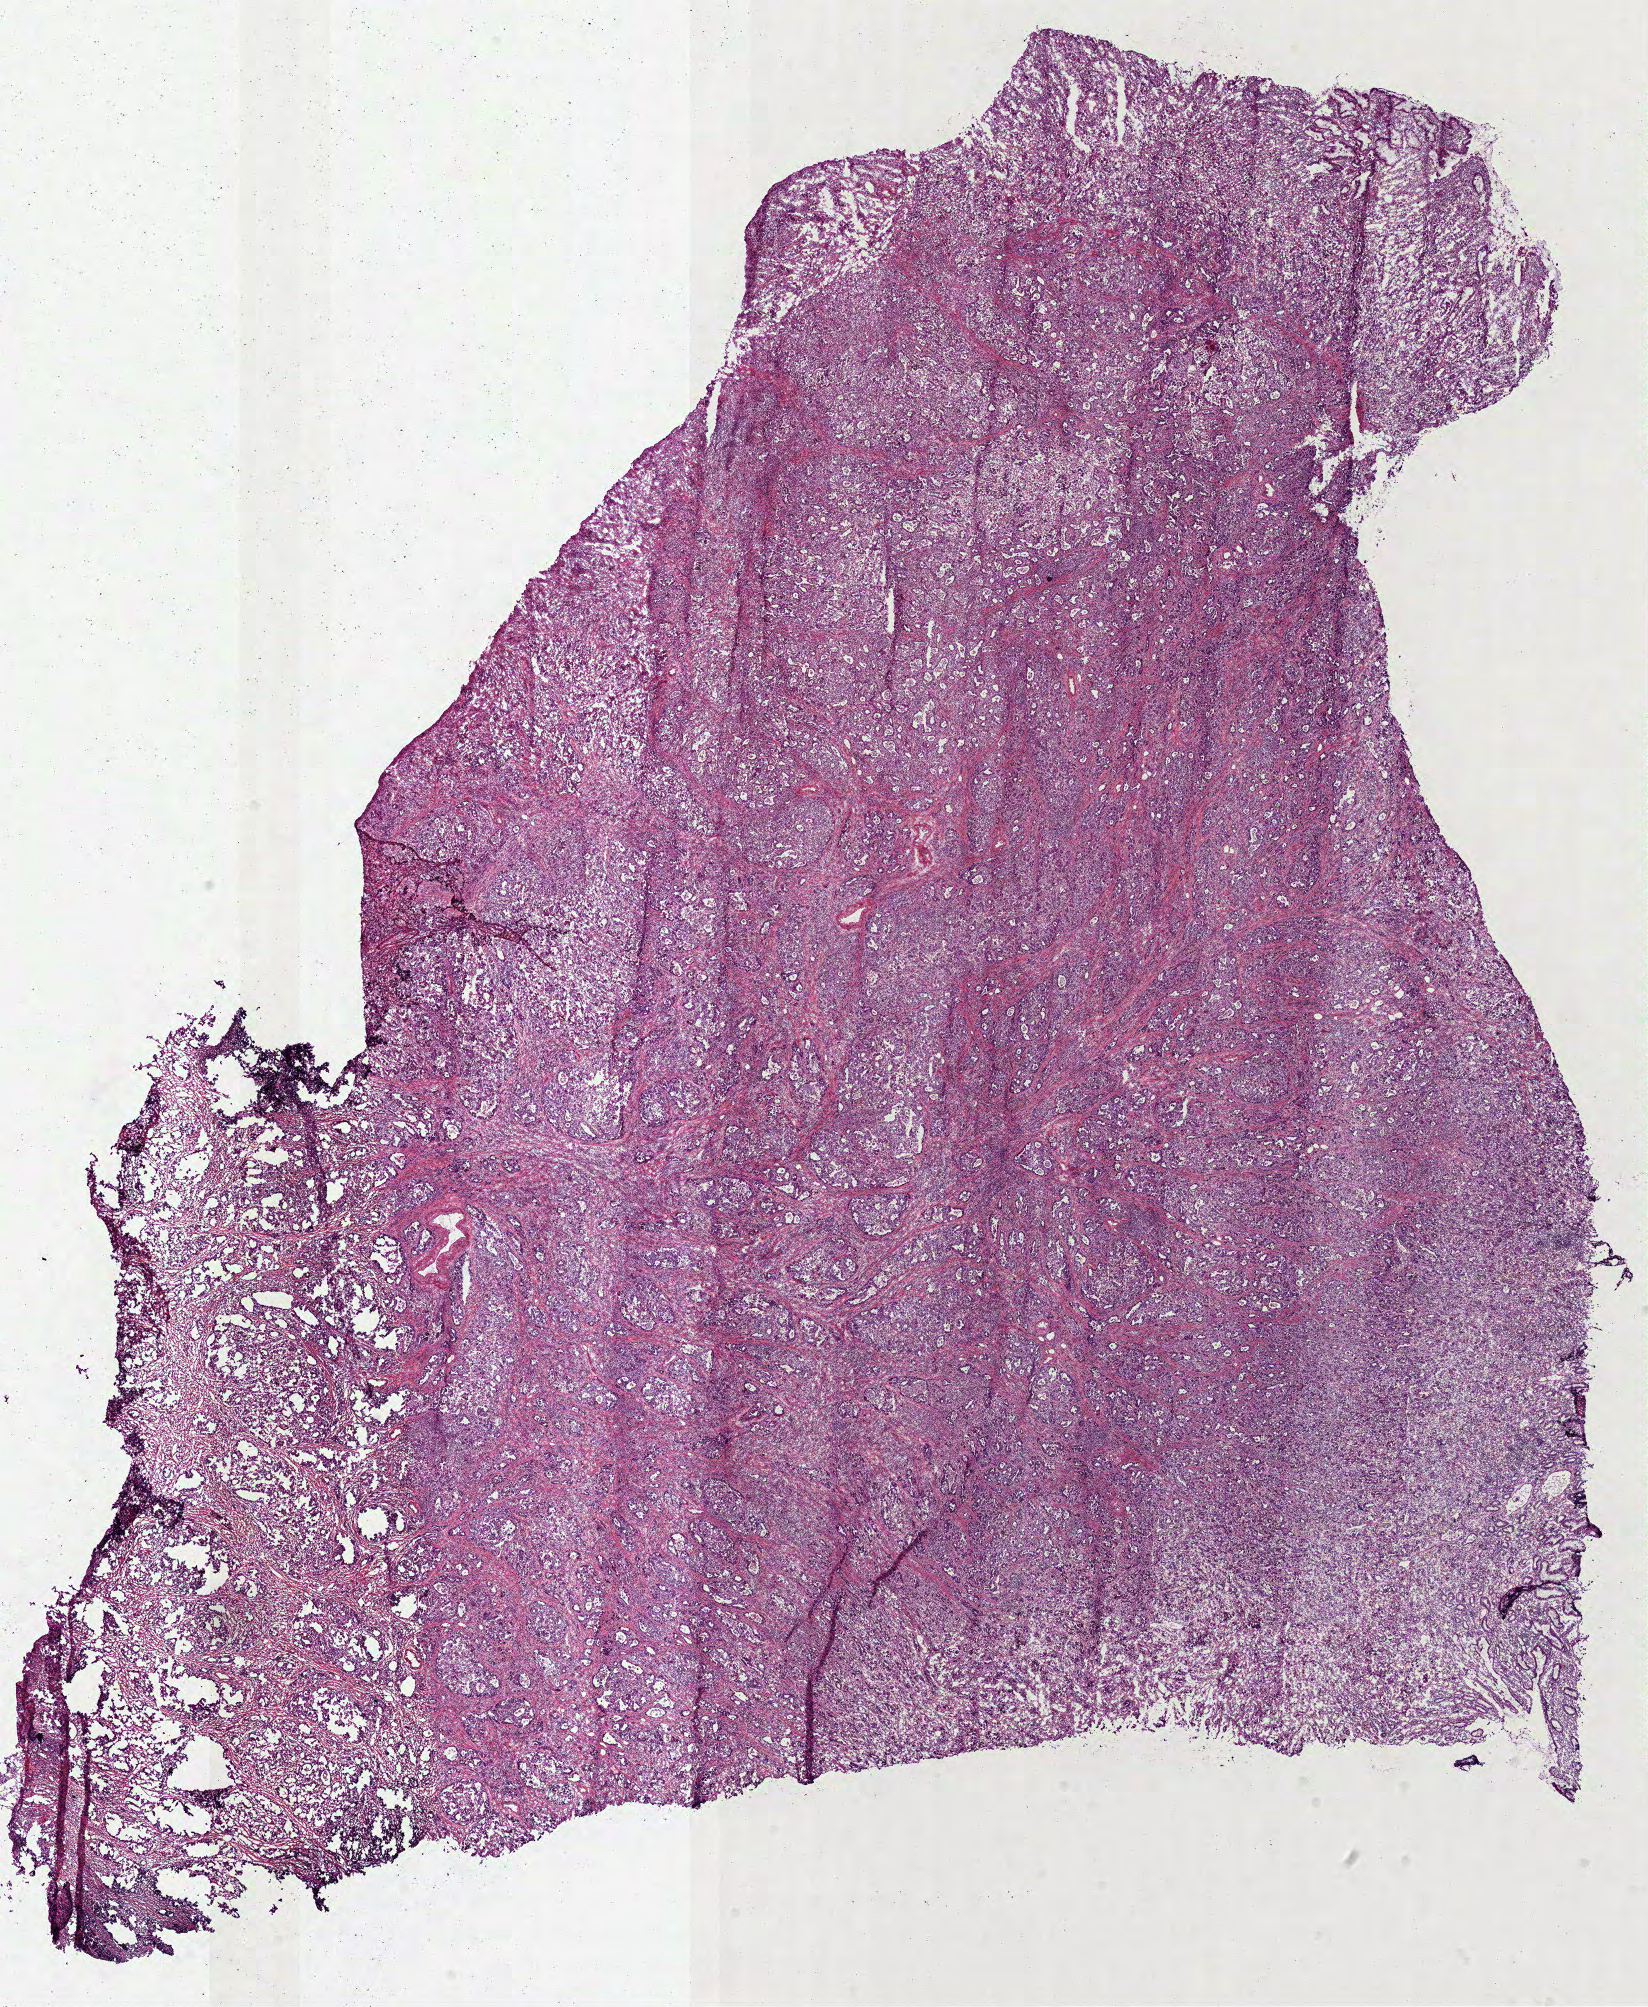
H&E-stained whole-slide image, shown as a low-resolution overview of the whole scanned area (about 13.3 x 16.2 mm, from a 40x scan). Frozen section from the bottom of the tissue portion. Stomach, primary tumour sample. Male patient; age at initial diagnosis 61 years. Histologic grade: G2 (moderately differentiated). Pathologist review of this section (percent, as recorded): tumour cells 100%, tumour nuclei 80%, normal cells 0%, stromal cells 0%, necrosis 0%. Inflammatory infiltration, as recorded: lymphocyte infiltration 18%, monocyte infiltration 0%, neutrophil infiltration 2%.
Histologic diagnosis: Adenocarcinoma, NOS (fundus of stomach). AJCC pathologic stage: IIIA (7th edition).